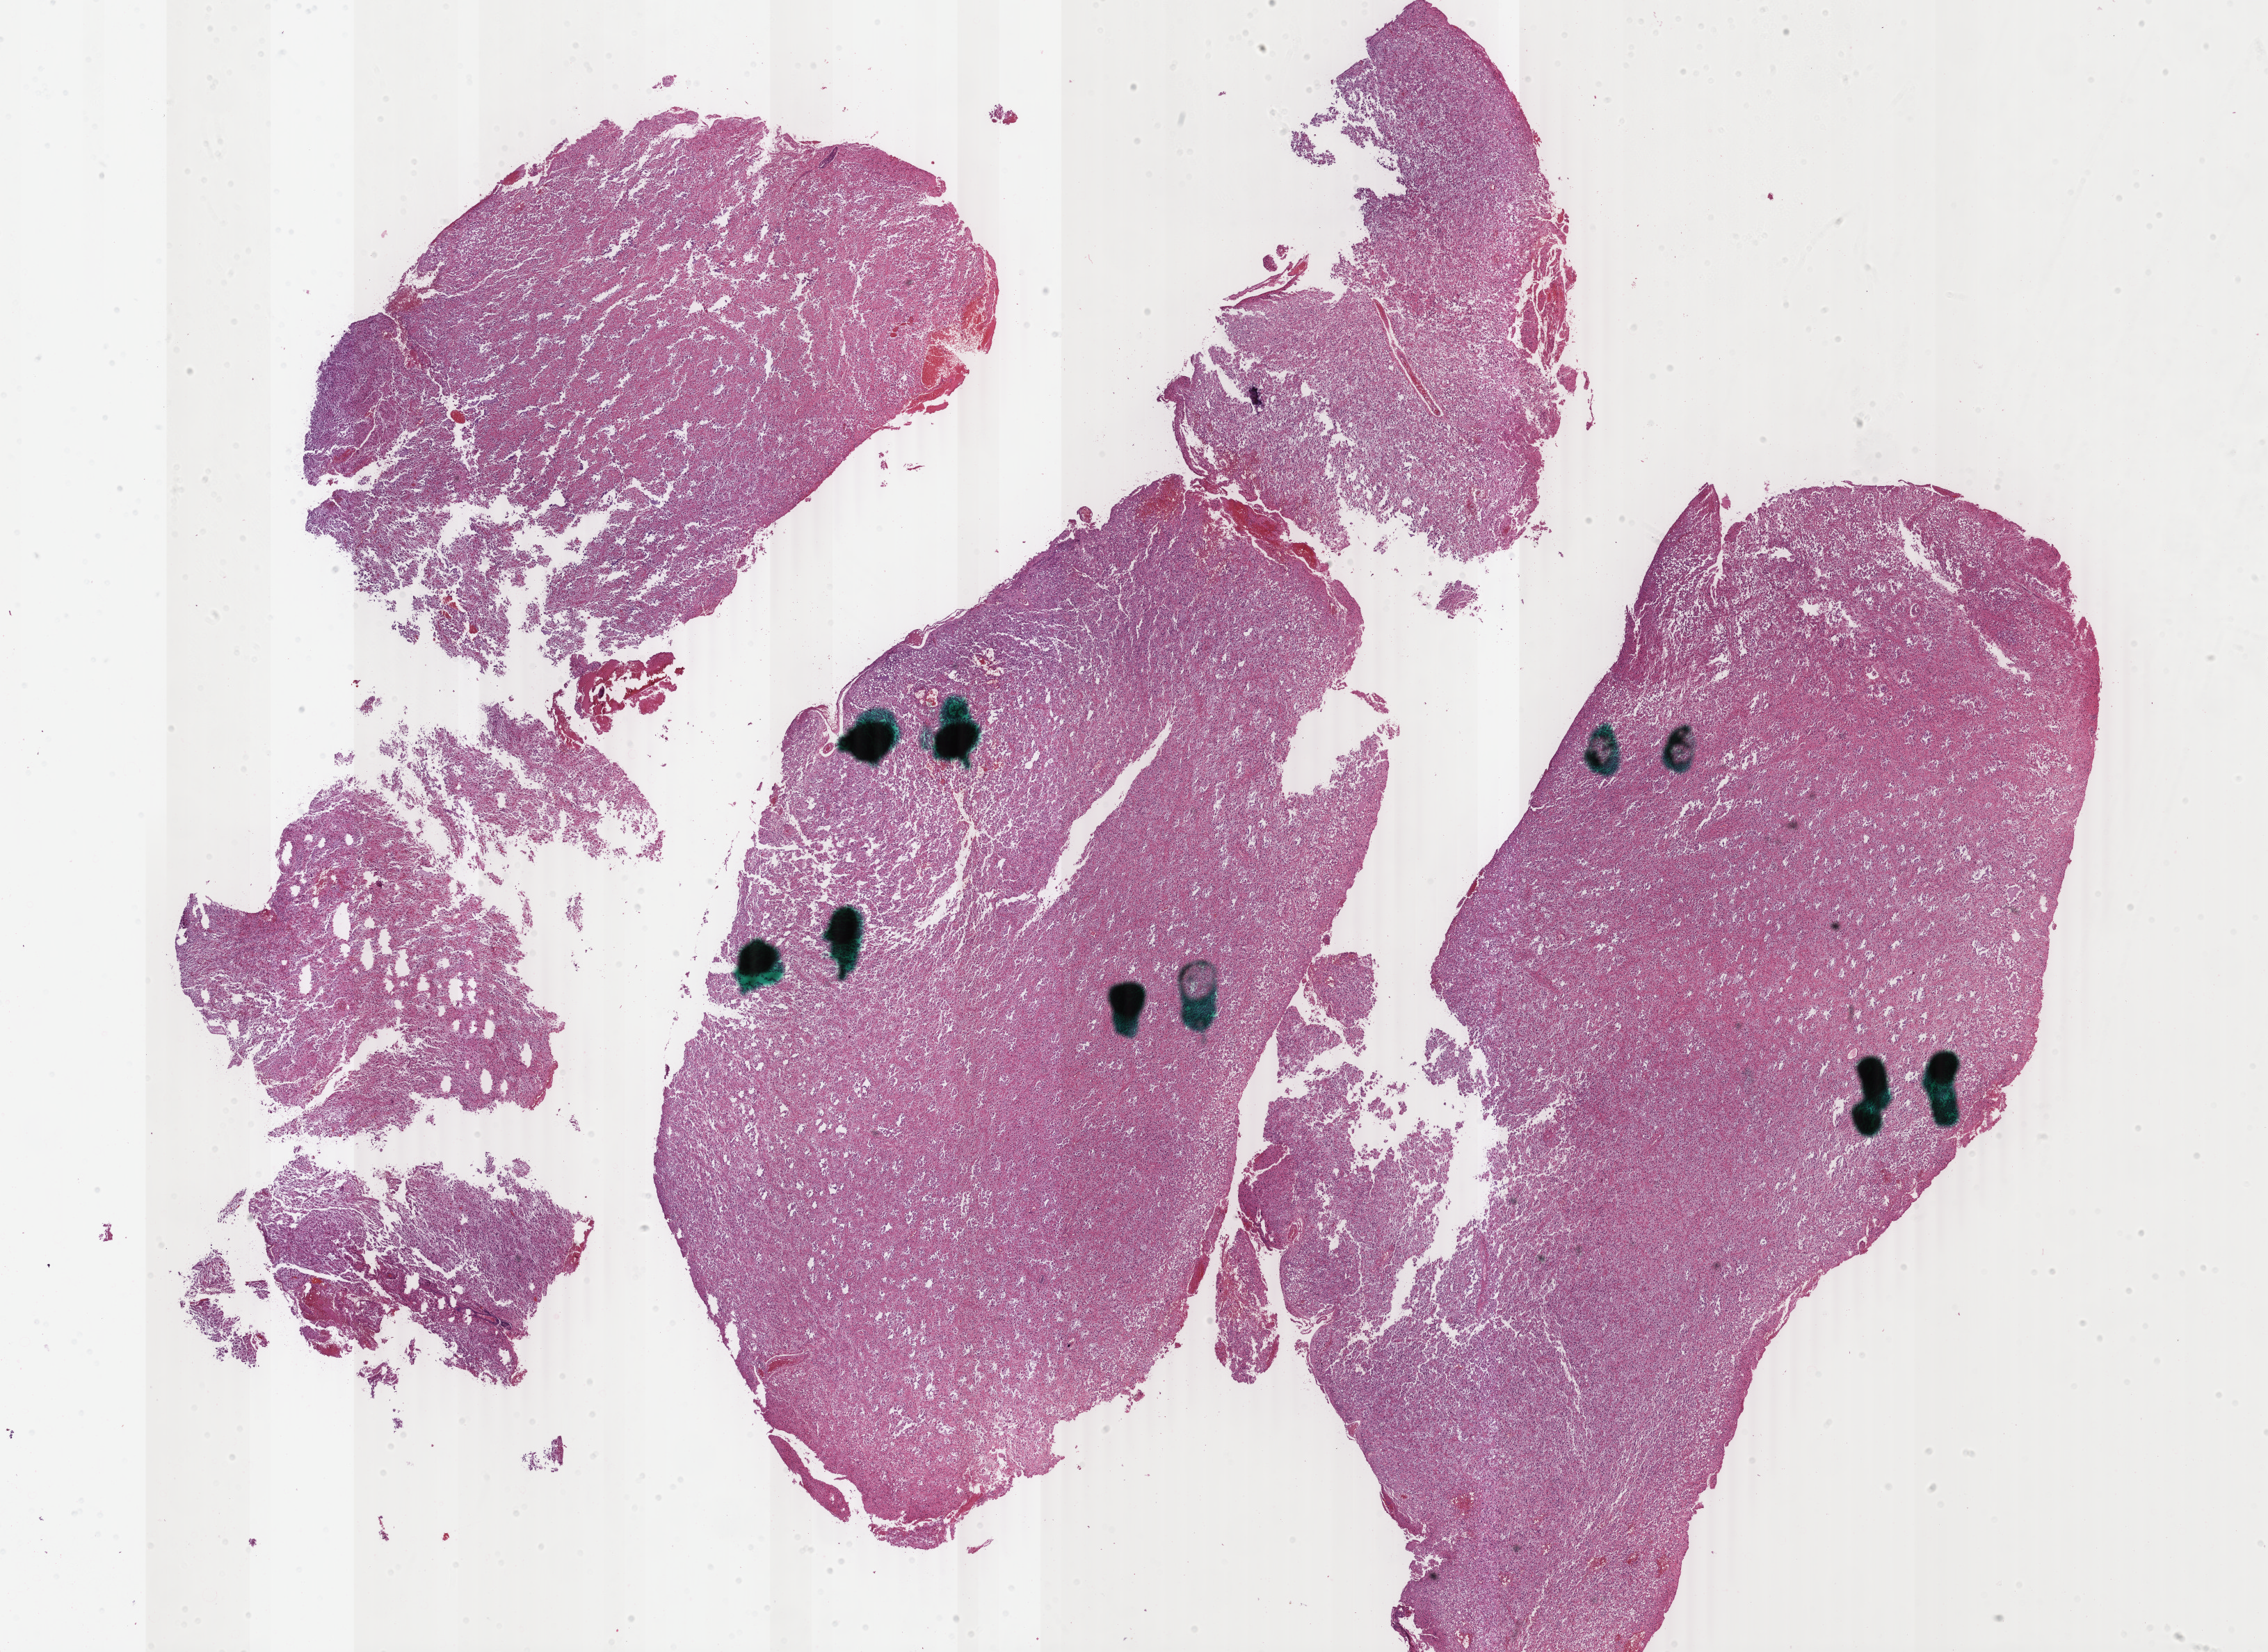
H&E-stained whole-slide image — whole scanned area (about 25.9 x 18.9 mm, from a 40x scan) shown as a low-resolution overview; formalin-fixed paraffin-embedded (FFPE) diagnostic section; primary tumour sample from the brain. Male patient; age at initial diagnosis 52 years.
Histologic diagnosis: Astrocytoma, anaplastic (cerebrum).